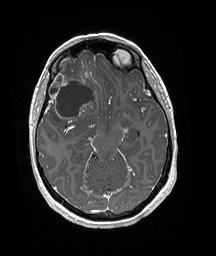
Brain MRI from a brain-tumour surgery series, one axial slice; position 115 of 192 along the scan axis; T1-weighted post-contrast; 1 mm slice thickness; 216 × 256 image matrix, field of view 211 × 250 mm. From the clinical record (not read from this slice): histopathology: Oligodendroglioma; WHO grade: 3; IDH mutation: yes; tumour location: Right Frontal.
Structures marked on this image (outlined manually by an expert reader):
- tumour: box from (x=47, y=58) to (x=97, y=124) px